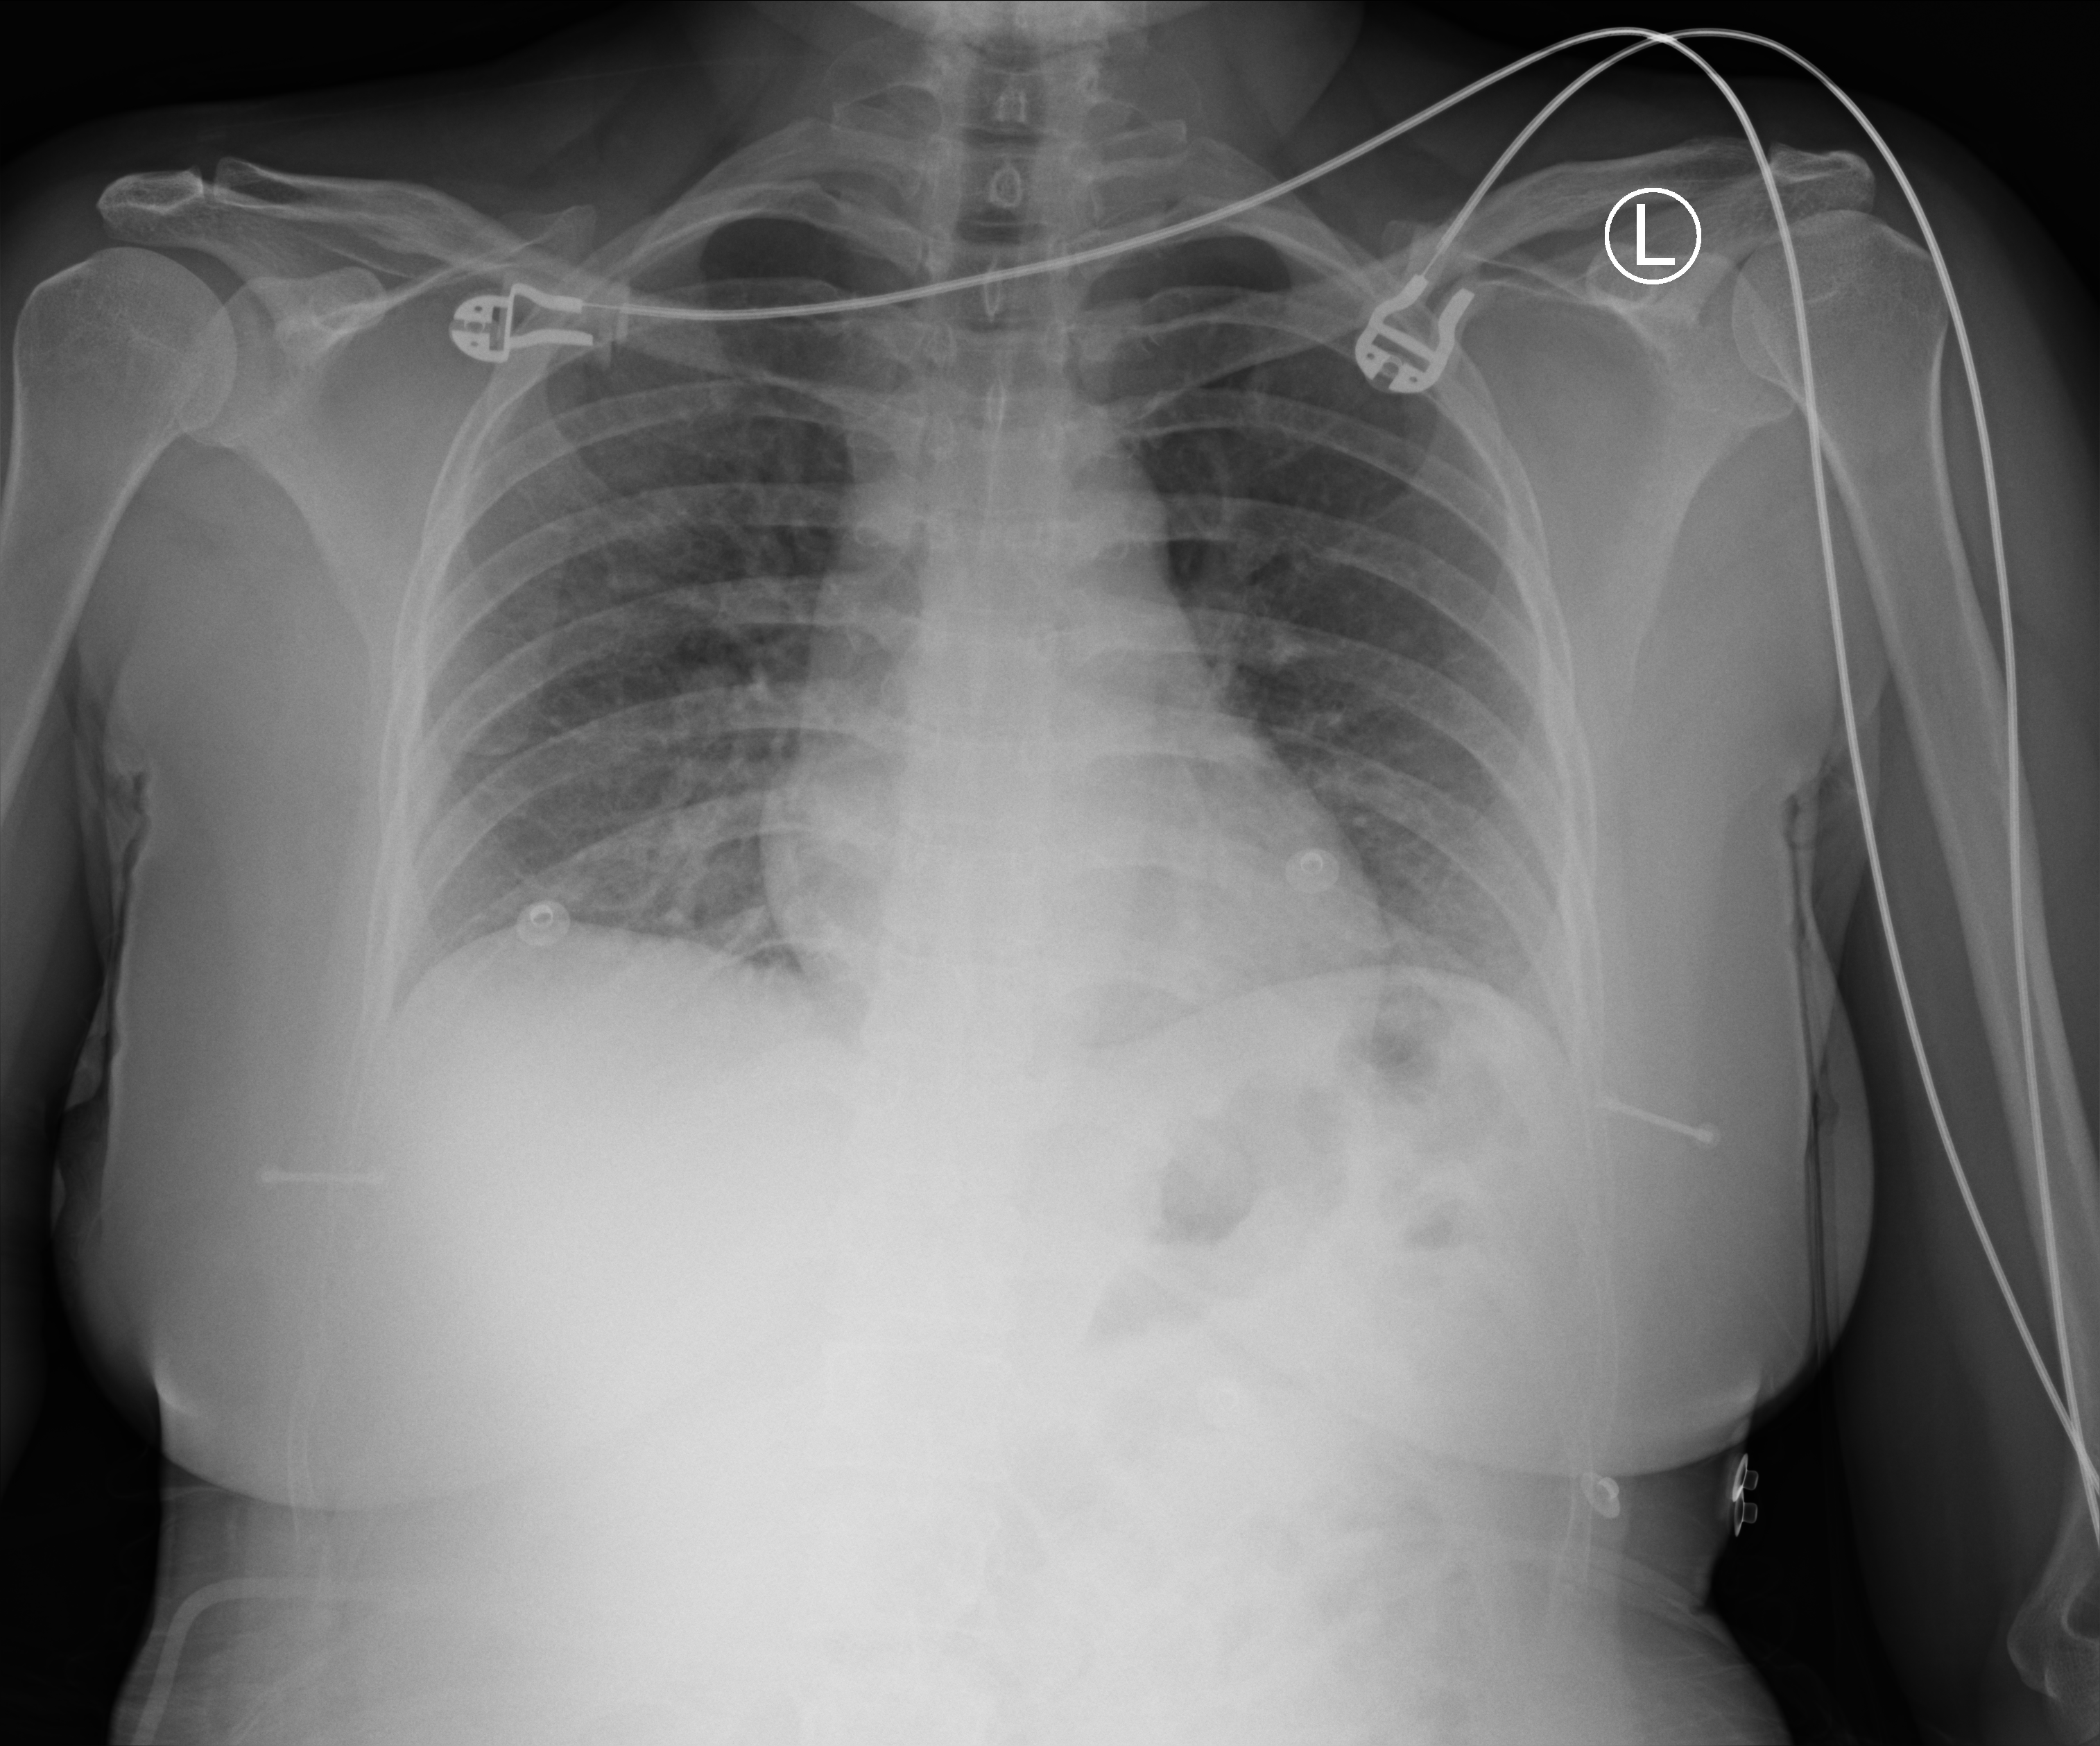
Bedside chest radiograph (computed radiography). Female patient hospitalised with COVID-19, age 18–59 years.
Hospital-stay facts (about this admission, not read from this image; timing relative to this image not recorded):
- mechanically ventilated during this hospital stay: no
- length of hospital stay: 2 days
- admitted to intensive care during this hospital stay: no